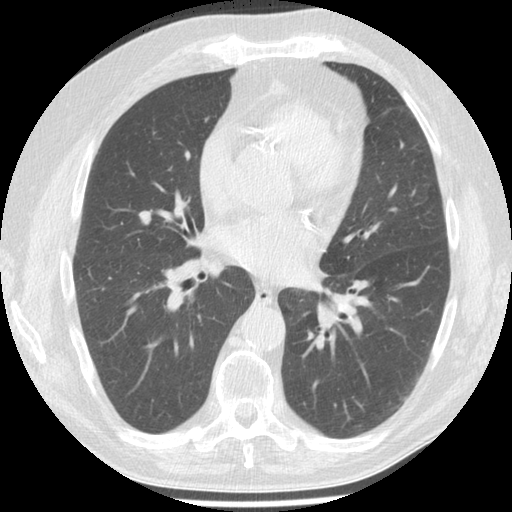
Low-dose screening chest CT, one axial slice. Slice 71 of 149 in the series (ordered by position). Reconstruction kernel STANDARD. 120 kVp. Lung window (W 1500 / L -600 HU). 2.5 mm slice thickness. 512 × 512 image matrix, field of view 340 × 340 mm.
Annotated regions visible in this slice (manually delineated by an expert):
- lesion 1 (tumor, middle lobe of right lung): bounding box [x1, y1, x2, y2] px = [138, 210, 152, 225]